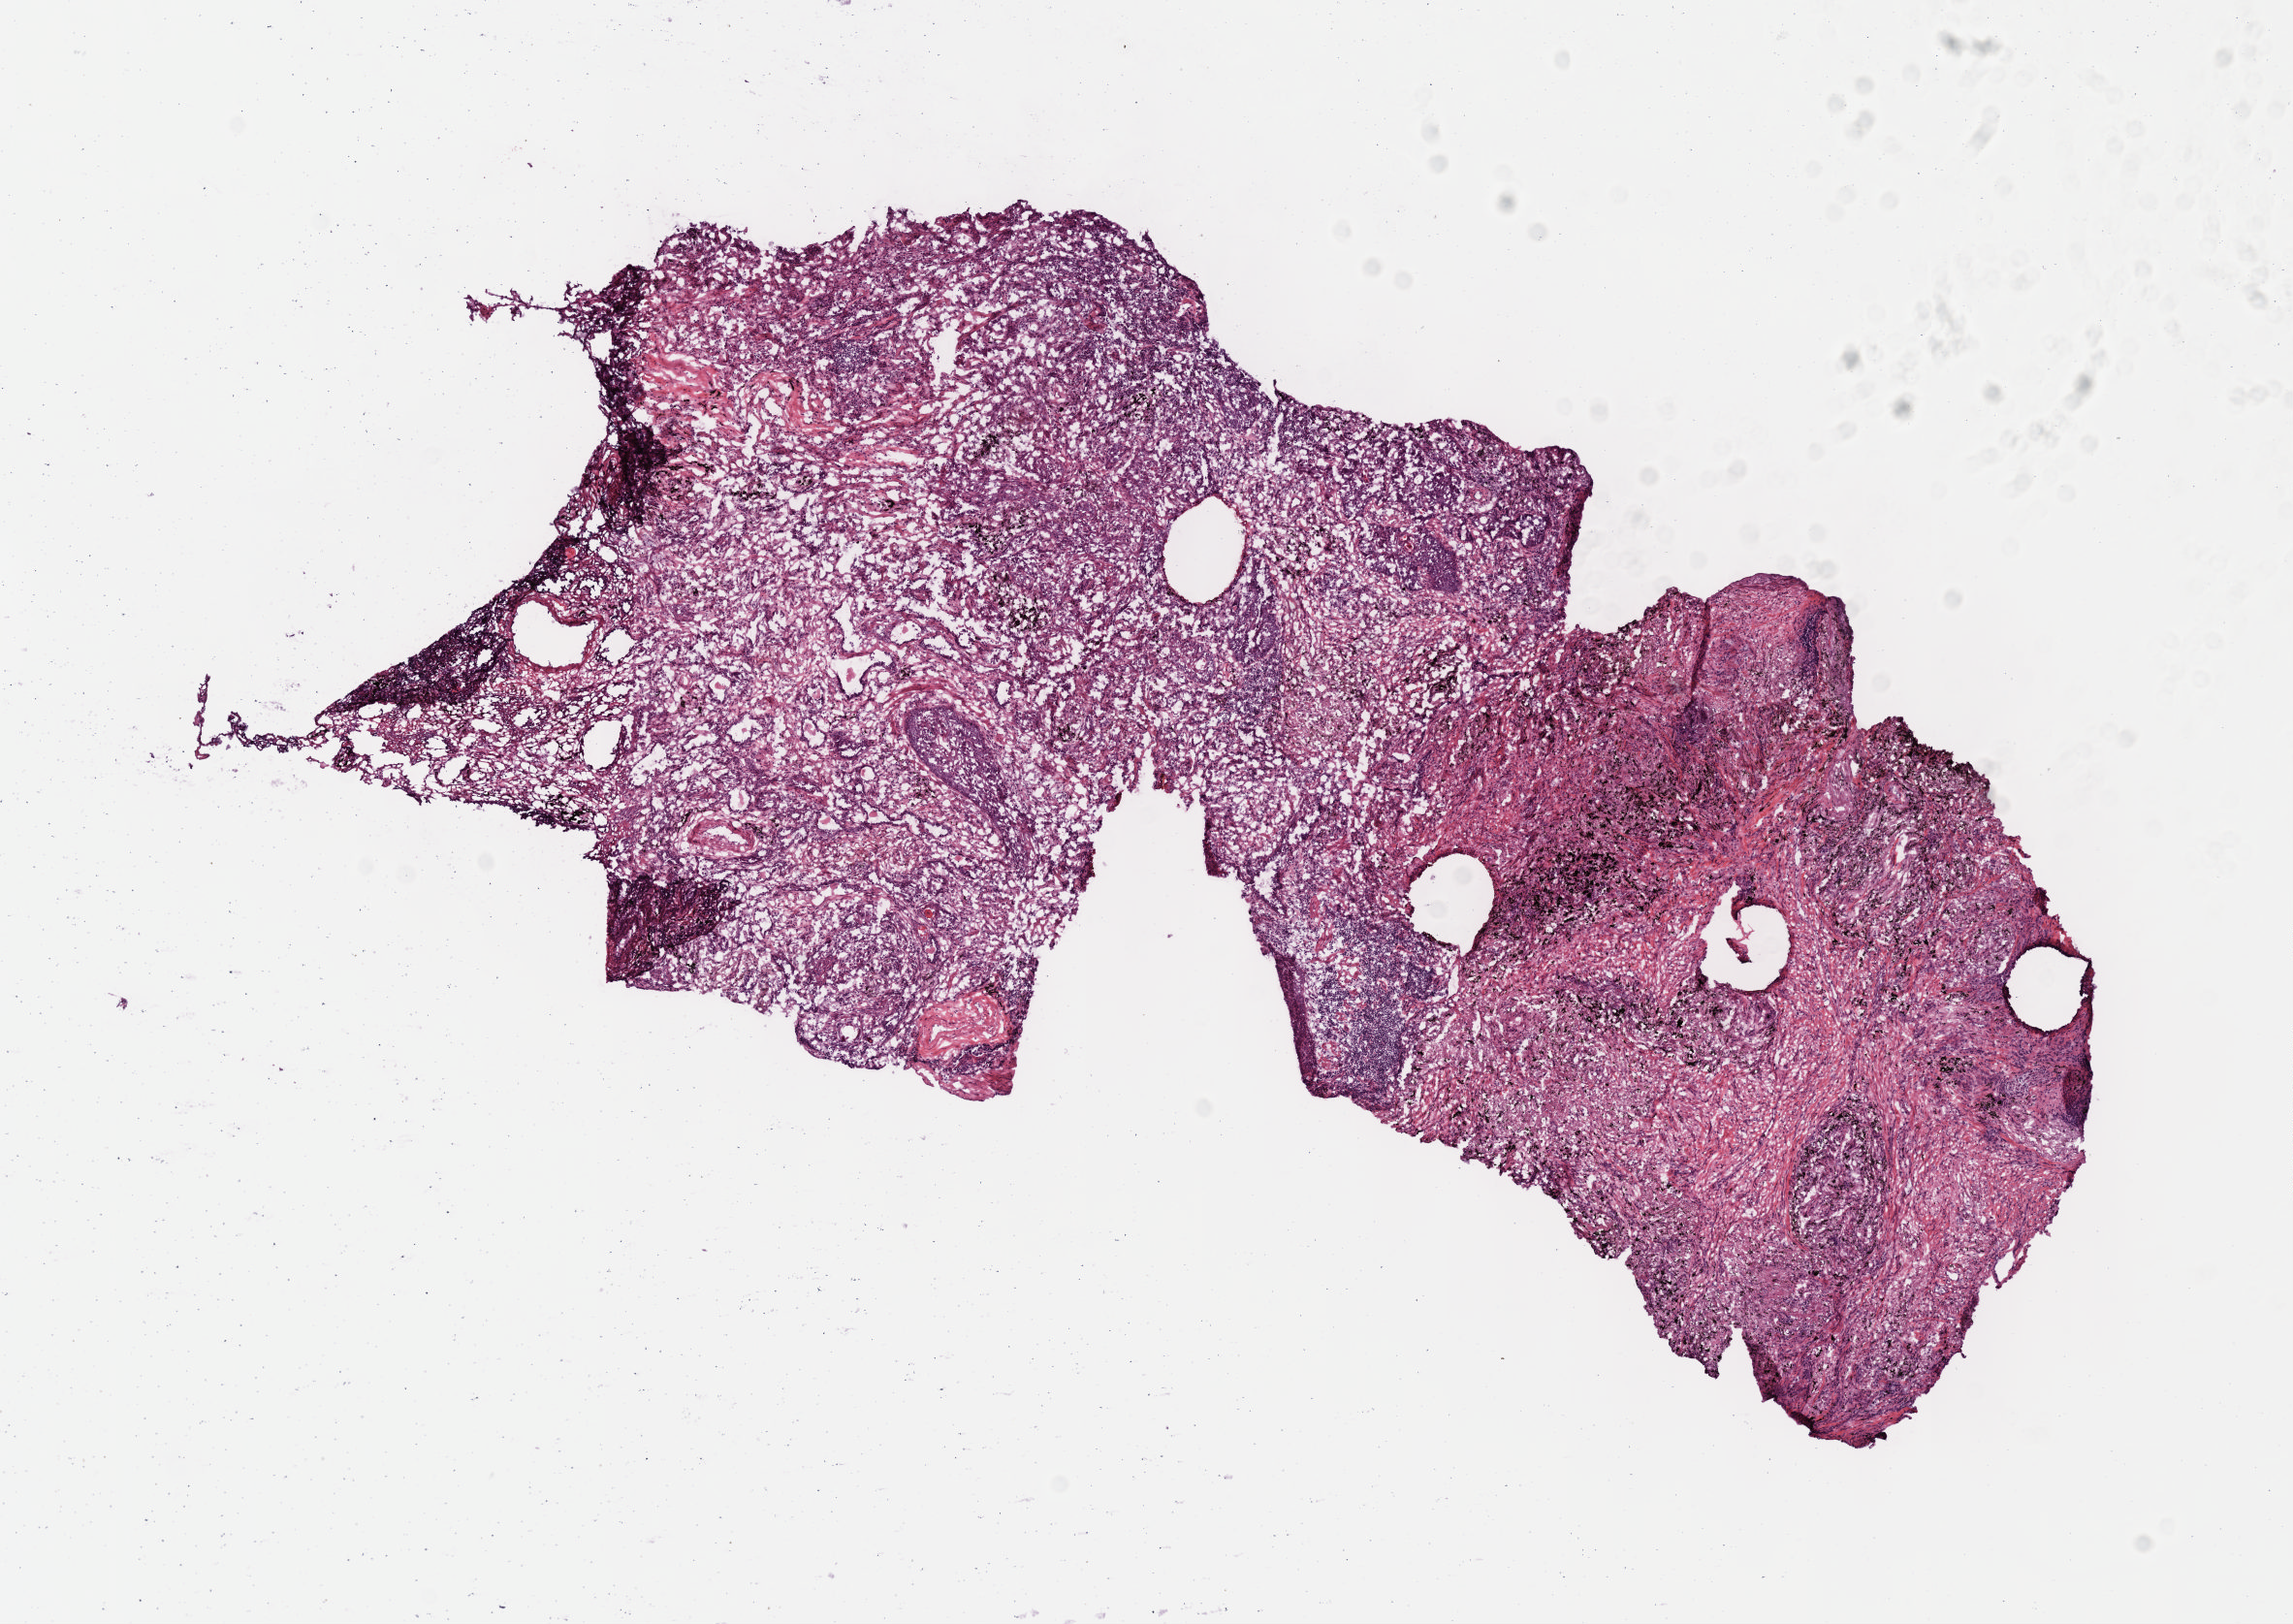
Digitized H&E-stained tissue section (whole slide) — whole scanned area (about 9.6 x 6.8 mm, slide scanned at 40x) shown as a low-resolution overview; frozen section; primary tumour sample from the lung. Patient: male, age at initial diagnosis 61 years. Composition of this section per pathologist review: tumour cells 100%, tumour nuclei 65%, normal cells 0%, stromal cells 0%, necrosis 0%. Infiltration values recorded for this section: lymphocyte infiltration 20%, monocyte infiltration 5%, neutrophil infiltration 0%.
• TNM: T1a N0 M0
• laterality: right
• AJCC pathologic stage: IA
• pathologic diagnosis: Squamous cell carcinoma, NOS (upper lobe, lung)